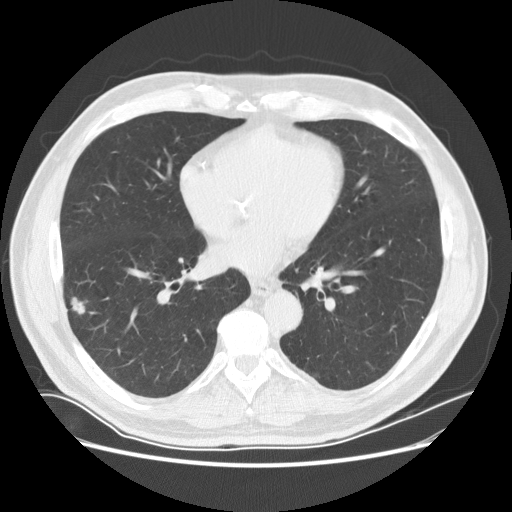
Low-dose screening chest CT, axial slice, baseline screening round, lung window (W 1500 / L -600 HU), 2.5 mm slice thickness, 120 kVp, slice 94 of 170 in the series, 512 × 512 image matrix, field of view 380 × 380 mm. Male, age 72 years at enrolment.
Expert reader's lesion annotation, bounding box [x1, y1, x2, y2] px = [59, 292, 92, 324]. The exam's reader record, not a measurement of the box and not confirmed to be the same lesion: non-calcified nodule or mass ≥4 mm, right lower lobe, 13 × 8 mm, poorly defined margins, soft tissue attenuation.